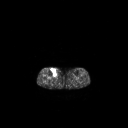
FDG PET of an extremity soft-tissue mass (from a PET/CT study), one axial slice; slice 141 of 267 in the series (ordered by position); 3.27 mm slice thickness; 128 × 128 image matrix, field of view 700 × 700 mm. Patient: female, 65 years. From the clinical record (not read from this slice): histological type: undifferentiated – high grade; grade: high; site of the primary tumour: right thigh.
Outlined on this slice (expert contour drawn on MRI and transferred to this co-registered scan by the dataset authors):
- gross tumour volume (mass): box from (x=50, y=68) to (x=57, y=75) px